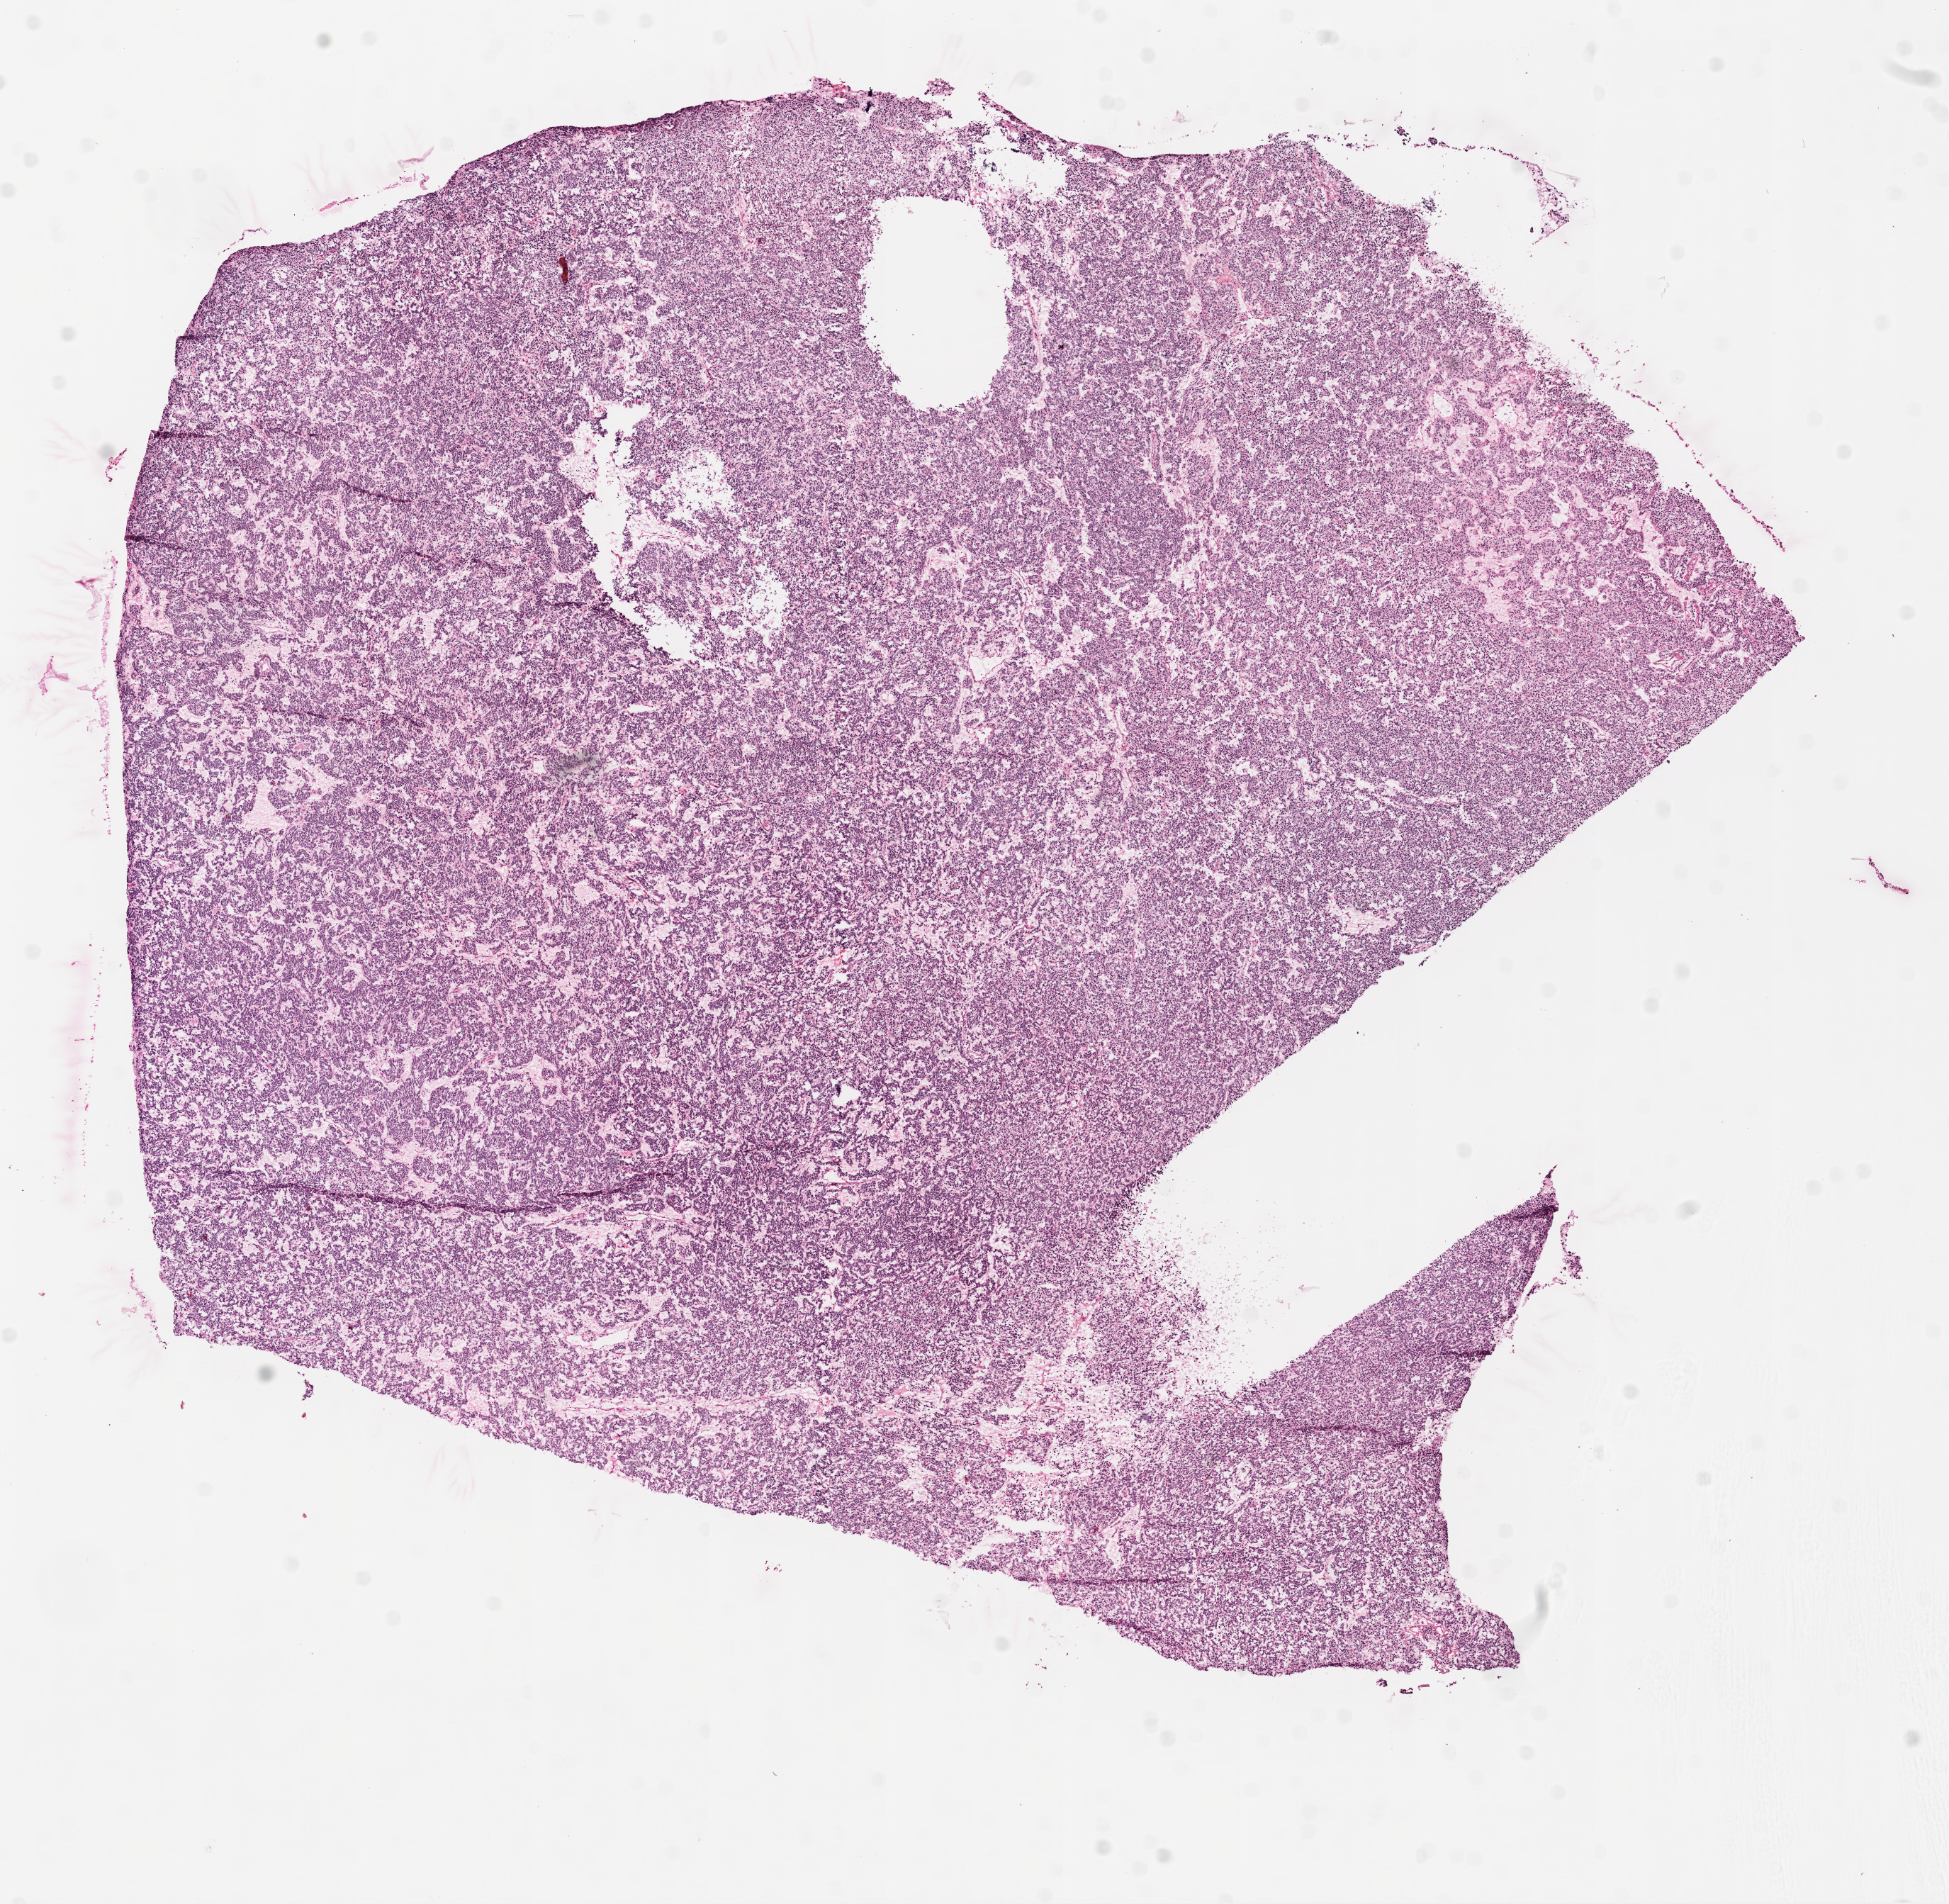
Whole-slide histology image, Hematoxylin and eosin (H&E) stained, low-resolution overview of the scanned area, about 11.0 x 10.8 mm (from a 20x scan). Frozen section. Sample: primary tumour, lung. Female patient; age at initial diagnosis 52 years. Composition of this section per pathologist review: tumour cells 90%, tumour nuclei 85%, normal cells 0%, stromal cells 10%, necrosis 0%.
• diagnosis: Squamous cell carcinoma, NOS (middle lobe, lung)
• AJCC pathologic stage: IA (7th edition)